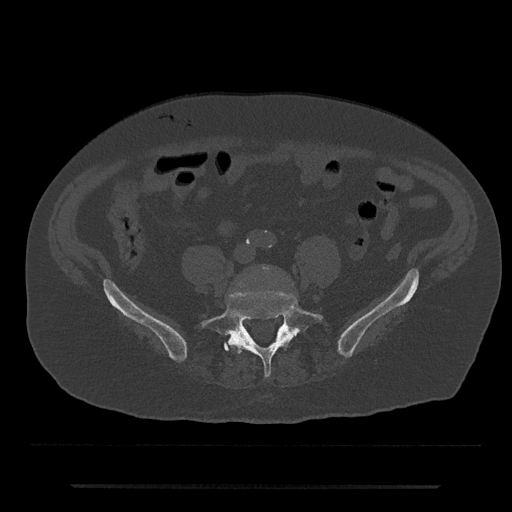
CT including the spine, one axial slice. Slice 297 of 797 in the series (ordered by position). Bone window (W 1800 / L 400 HU). 0.5 mm slice thickness. 512 × 512 image matrix. Male patient, age 80 years. From the clinical record (not read from this slice): primary cancer: prostate; vertebrae with lytic lesions (as recorded): L1, T11.
Outlined on this slice (semi-automatic segmentation, software-assisted and operator-edited):
- L4 vertebra: bounding box (x1, y1, x2, y2) in pixels: (261, 266, 270, 271)
- L5 vertebra: (201, 291, 323, 378)